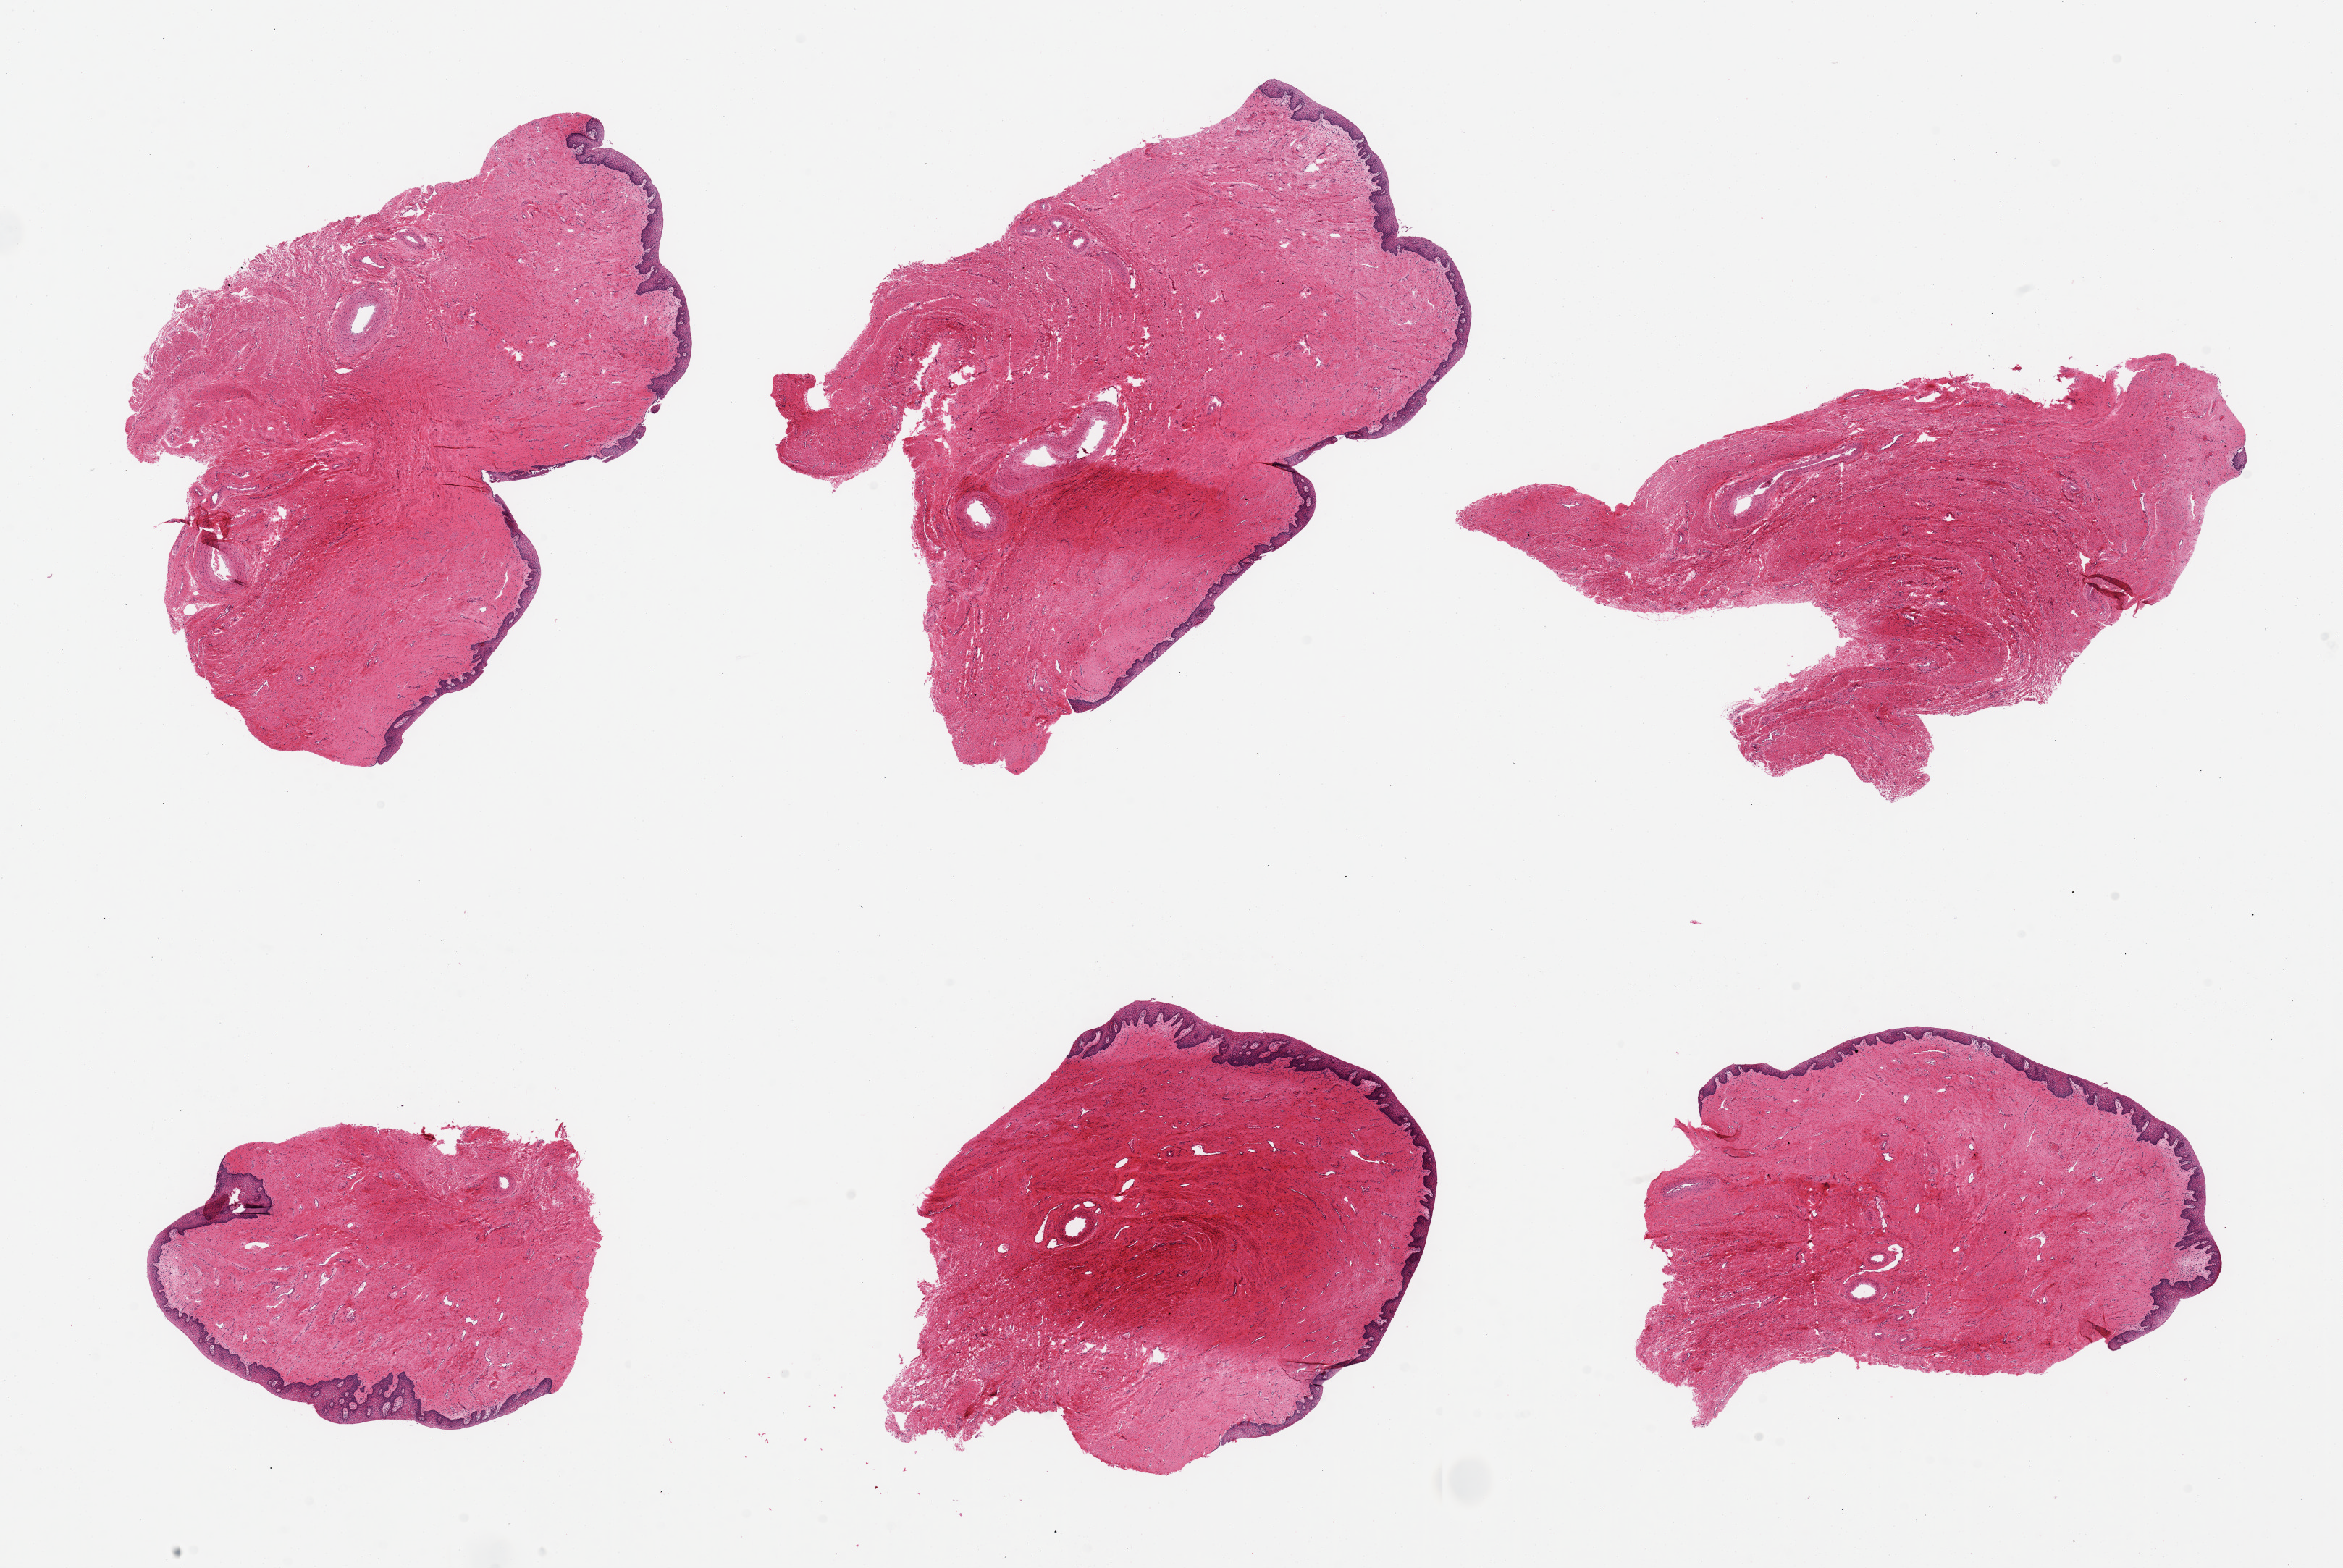
Digitized hematoxylin and eosin (H&E)-stained section, brightfield — shown as a low-resolution overview of the whole scanned area (about 25.6 x 17.1 mm). PAXgene-fixed paraffin-embedded (PFPE) section. Target tissue: vagina. Donor tissue sample. Donor sex: female.
Pathologist's review note for this sample: 6 pieces, squamous mucosa up to ~0.15mm.